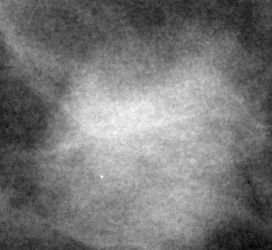
Crop from a digitized film mammogram around one marked abnormality; right breast; MLO view; BI-RADS breast density category 2 (scale 1–4).
- Marked abnormality: mass, shape round, margins ill defined; BI-RADS assessment category 4; pathology (as recorded): malignant.